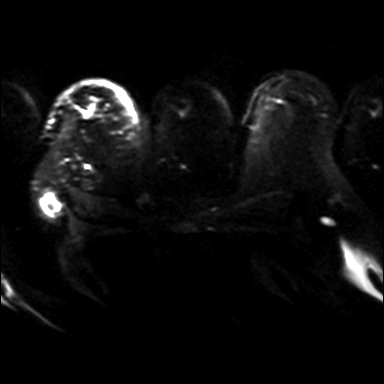
Breast MRI, one axial slice; position 27 of 36 along the scan axis; diffusion-weighted series; image 2 of 4 stored at this slice position (different b-values; order by instance number); 3 T; 384 × 384 image matrix. Female patient.
Annotated regions visible in this slice (manually delineated by an expert):
- tumour on diffusion-weighted imaging: box from (x=84, y=110) to (x=91, y=116) px